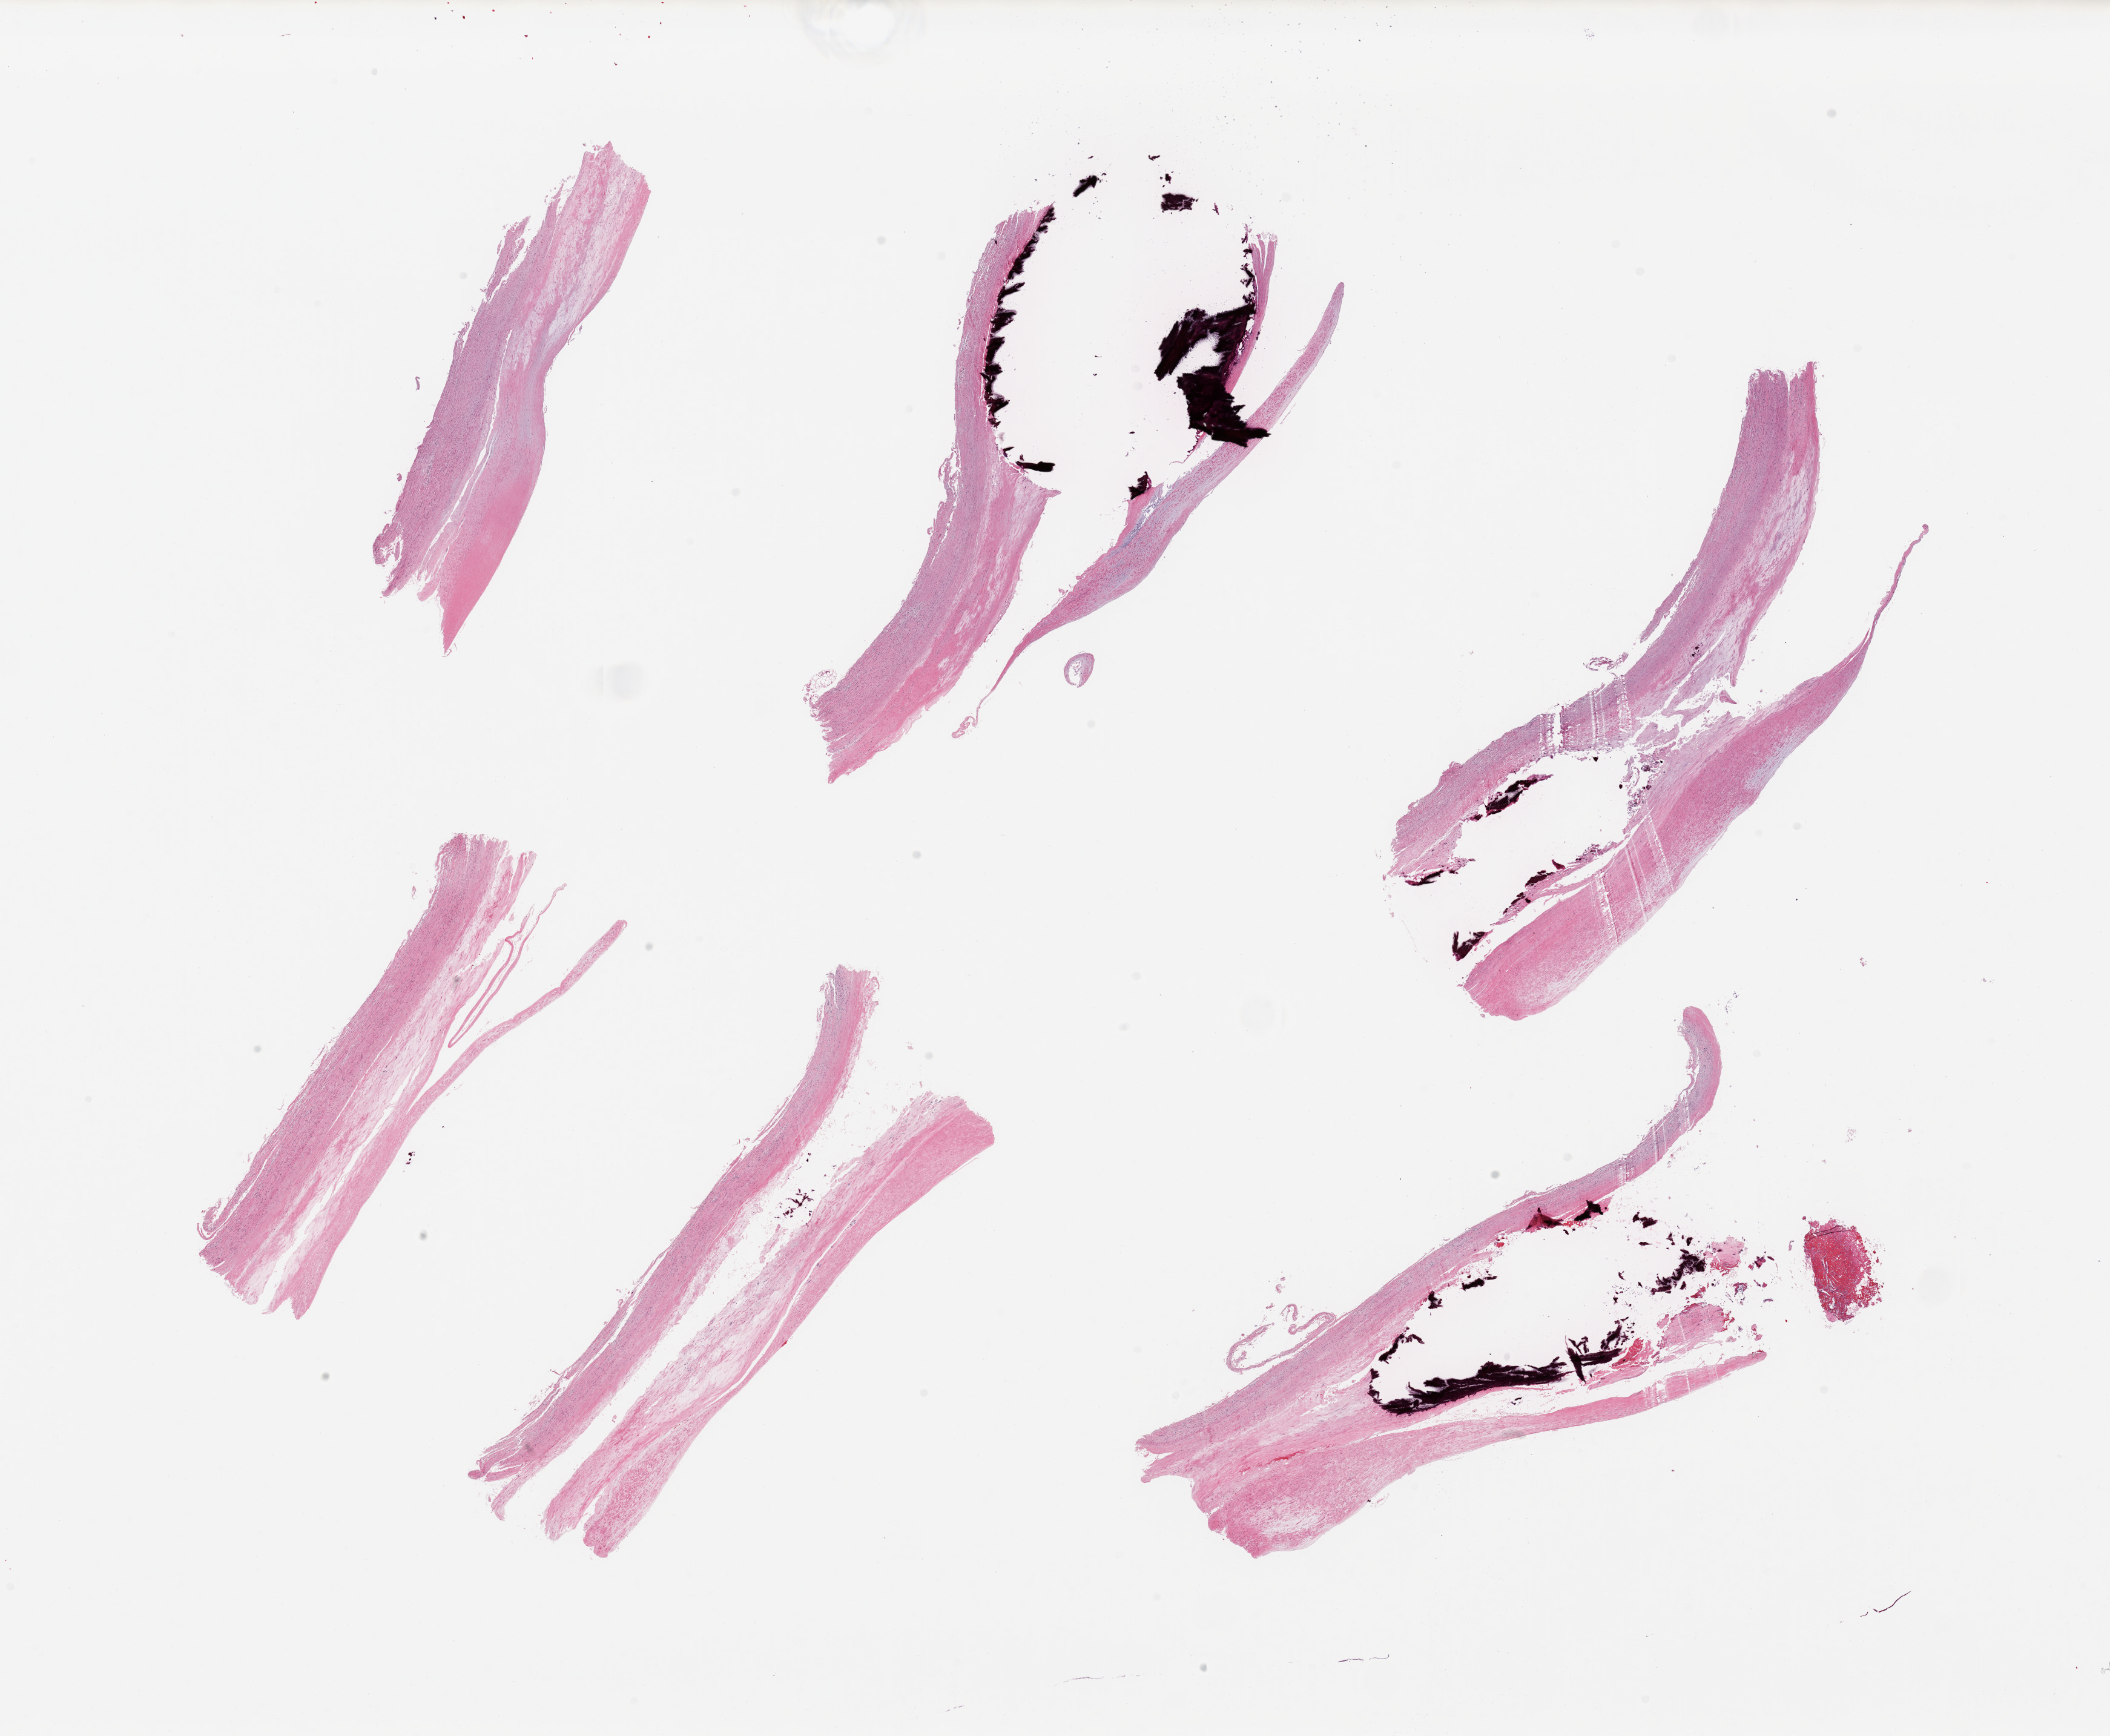
Digitized haematoxylin and eosin-stained section, whole scanned area (about 27.6 x 22.7 mm) shown as a low-resolution overview. PAXgene-fixed paraffin-embedded (PFPE) section. Section of aorta (target tissue). Tissue donor sample. Female donor.
Pathologist's review note for this sample: 6 pieces; large [4mm] calcified intramural deposit in 3 of 6 pieces; atheromatous plaques in all.